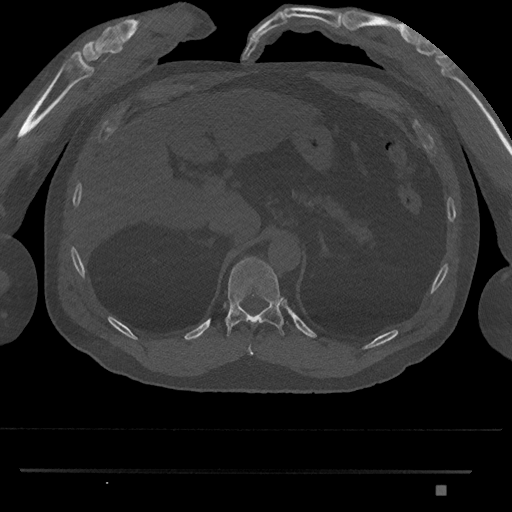
CT including the spine, one axial slice. Position 951 of 1134 along the scan axis. 120 kVp. Bone window (W 1800 / L 400 HU). 0.5 mm slice thickness. 512 × 512 image matrix, field of view 429 × 429 mm. Patient: male, 65 years. Case-level facts recorded for this patient, not image findings: primary cancer: prostate.
Structures marked on this image (semi-automatic segmentation, software-assisted and operator-edited):
- T10 vertebra: box from (x=247, y=345) to (x=253, y=355) px
- T11 vertebra: (x=225, y=256)–(x=288, y=337)